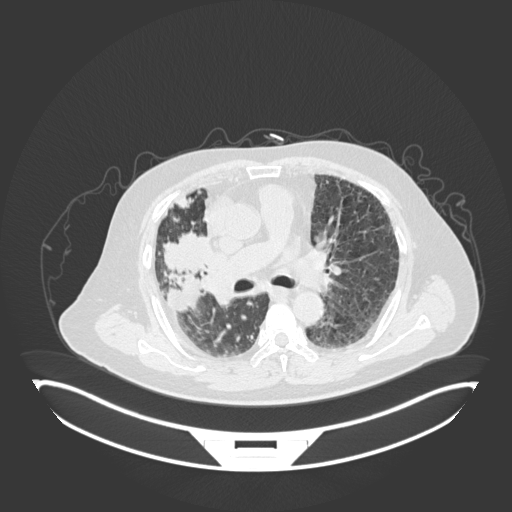
Chest CT, one axial slice. Slice 97 of 201 in the series (ordered by position). Lung window (W 1500 / L -600 HU). 1 mm slice thickness. 512 × 512 image matrix. Patient: male, 69 years. From the clinical record (not read from this slice): clinical TNM (as recorded): T4 N3 M1.
Structures marked on this image (rectangle marked by the reading radiologist):
- lung tumour (recorded histology: adenocarcinoma): bounding box [x1, y1, x2, y2] px = [158, 230, 215, 276]